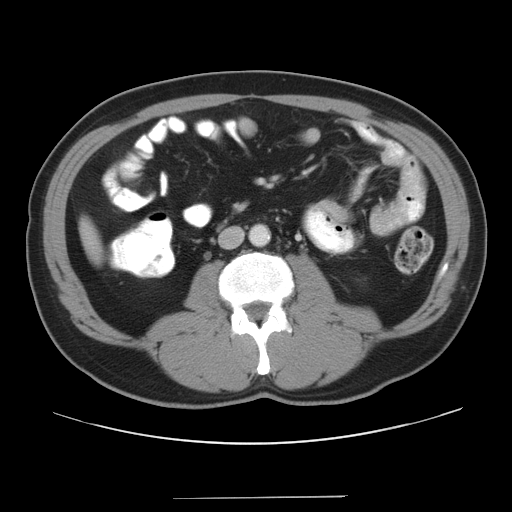
Contrast-enhanced abdominal CT, one axial slice. Position 10 of 37 along the scan axis. 120 kVp. Intravenous contrast given. Soft-tissue window (W 400 / L 40 HU). 512 × 512 image matrix, field of view 400 × 400 mm. Male patient, age 46 years. Case-level facts recorded for this patient, not image findings: diagnosis: colorectal cancer liver metastases, imaged before liver resection; multiple liver metastases: yes; largest metastasis: 1 cm.
Structures marked on this image (expert manual segmentation):
- liver: box from (x=94, y=253) to (x=100, y=254) px
- planned liver remnant (the part of the liver to remain after resection): (x=94, y=253)–(x=100, y=254)